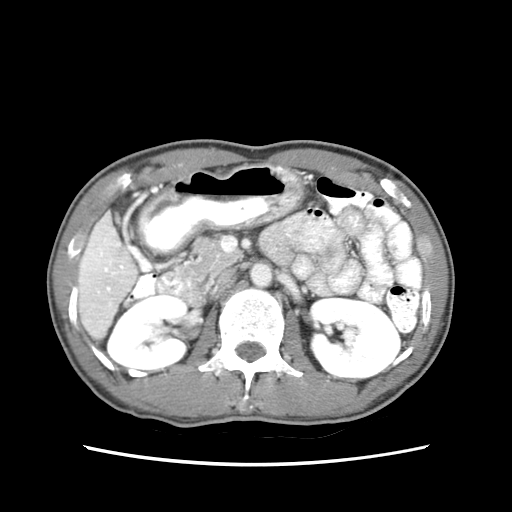
Contrast-enhanced abdominal CT (liver protocol), one axial slice; position 23 of 79 along the scan axis; reconstruction kernel STANDARD; soft-tissue window (W 400 / L 40 HU); 2.5 mm slice thickness; 512 × 512 image matrix, field of view 320 × 320 mm. Case-level facts recorded for this patient, not image findings: diagnosis: hepatocellular carcinoma (patient treated with transarterial chemoembolisation; whether this scan precedes or follows treatment is not stated here); TNM stage (as recorded): Stage-IIIB; Child-Pugh class: A; tumour differentiation: moderately differentiated; tumour nodularity: multinodular.
Annotated regions visible in this slice (semi-automatically segmented with operator editing):
- liver parenchyma outside the tumour (the mass and vessels are separate outlines, so this box may not span the whole liver): box from (x=76, y=211) to (x=136, y=338) px
- liver vessels: (x=84, y=226)–(x=125, y=308)